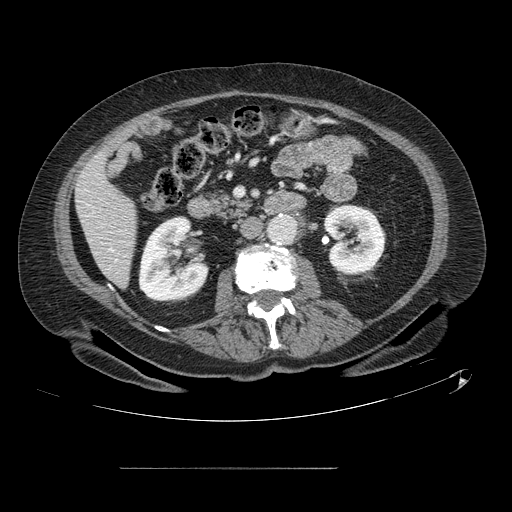
Contrast-enhanced abdominal CT, one axial slice; position 35 of 148 along the scan axis; 120 kVp; intravenous contrast given; soft-tissue window (W 400 / L 40 HU); 2.5 mm slice thickness; 512 × 512 image matrix, field of view 439 × 439 mm. Female patient, age 75 years. Case-level facts recorded for this patient, not image findings: diagnosis: colorectal cancer liver metastases, imaged before liver resection; multiple liver metastases: no; largest metastasis: 2.4 cm; disease in both lobes: no.
Outlined on this slice (manually delineated by an expert):
- liver: bounding box (x1, y1, x2, y2) in pixels: (76, 154, 136, 286)
- planned liver remnant (the part of the liver to remain after resection): (76, 154, 136, 286)